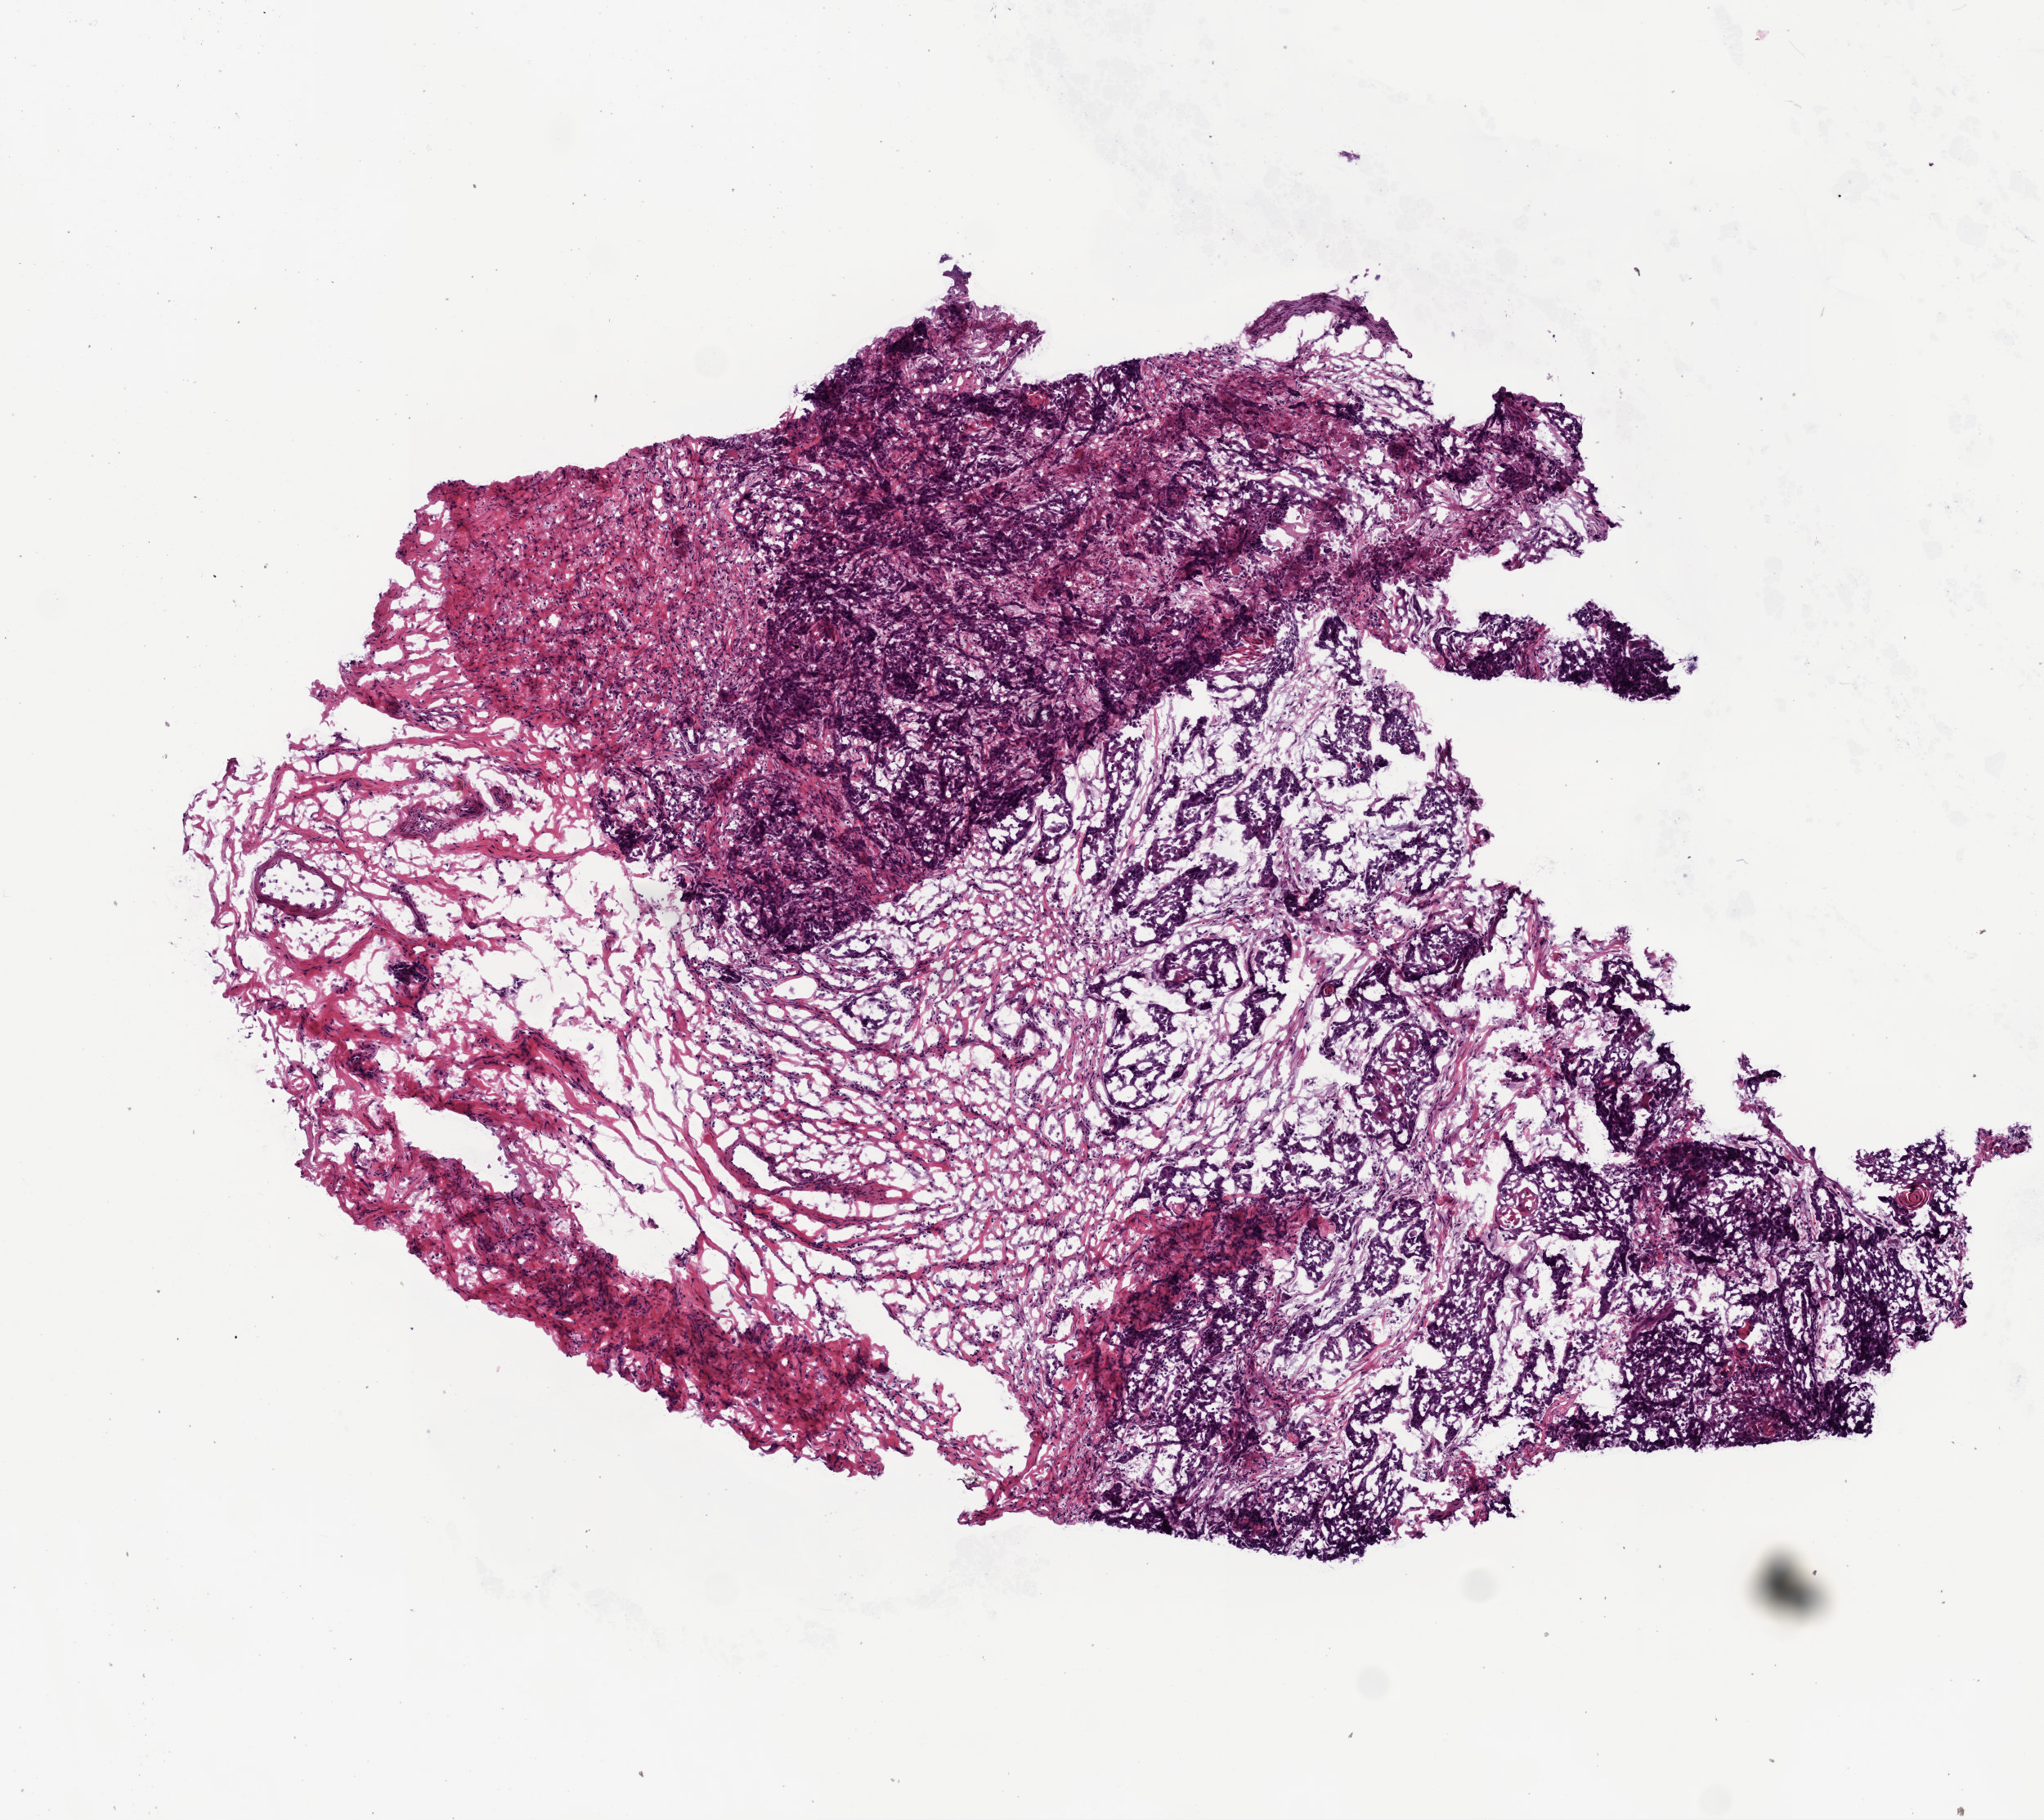
Digitized Hematoxylin and eosin (H&E) stained tissue section (whole slide), a low-resolution overview of the entire scanned area, about 5.0 x 4.5 mm; frozen section; primary tumour sample from the head and neck. Male patient; age at initial diagnosis 52 years. Histologic grade: G3 (poorly differentiated). Pathologist review of this section (percent, as recorded): tumour cells 50%, tumour nuclei 60%, normal cells 0%, stromal cells 50%, necrosis 0%.
Lymph nodes positive (case pathology): 42 of 47 examined. AJCC pathologic stage: IVA (7th edition). Pathologic diagnosis: Squamous cell carcinoma, NOS.